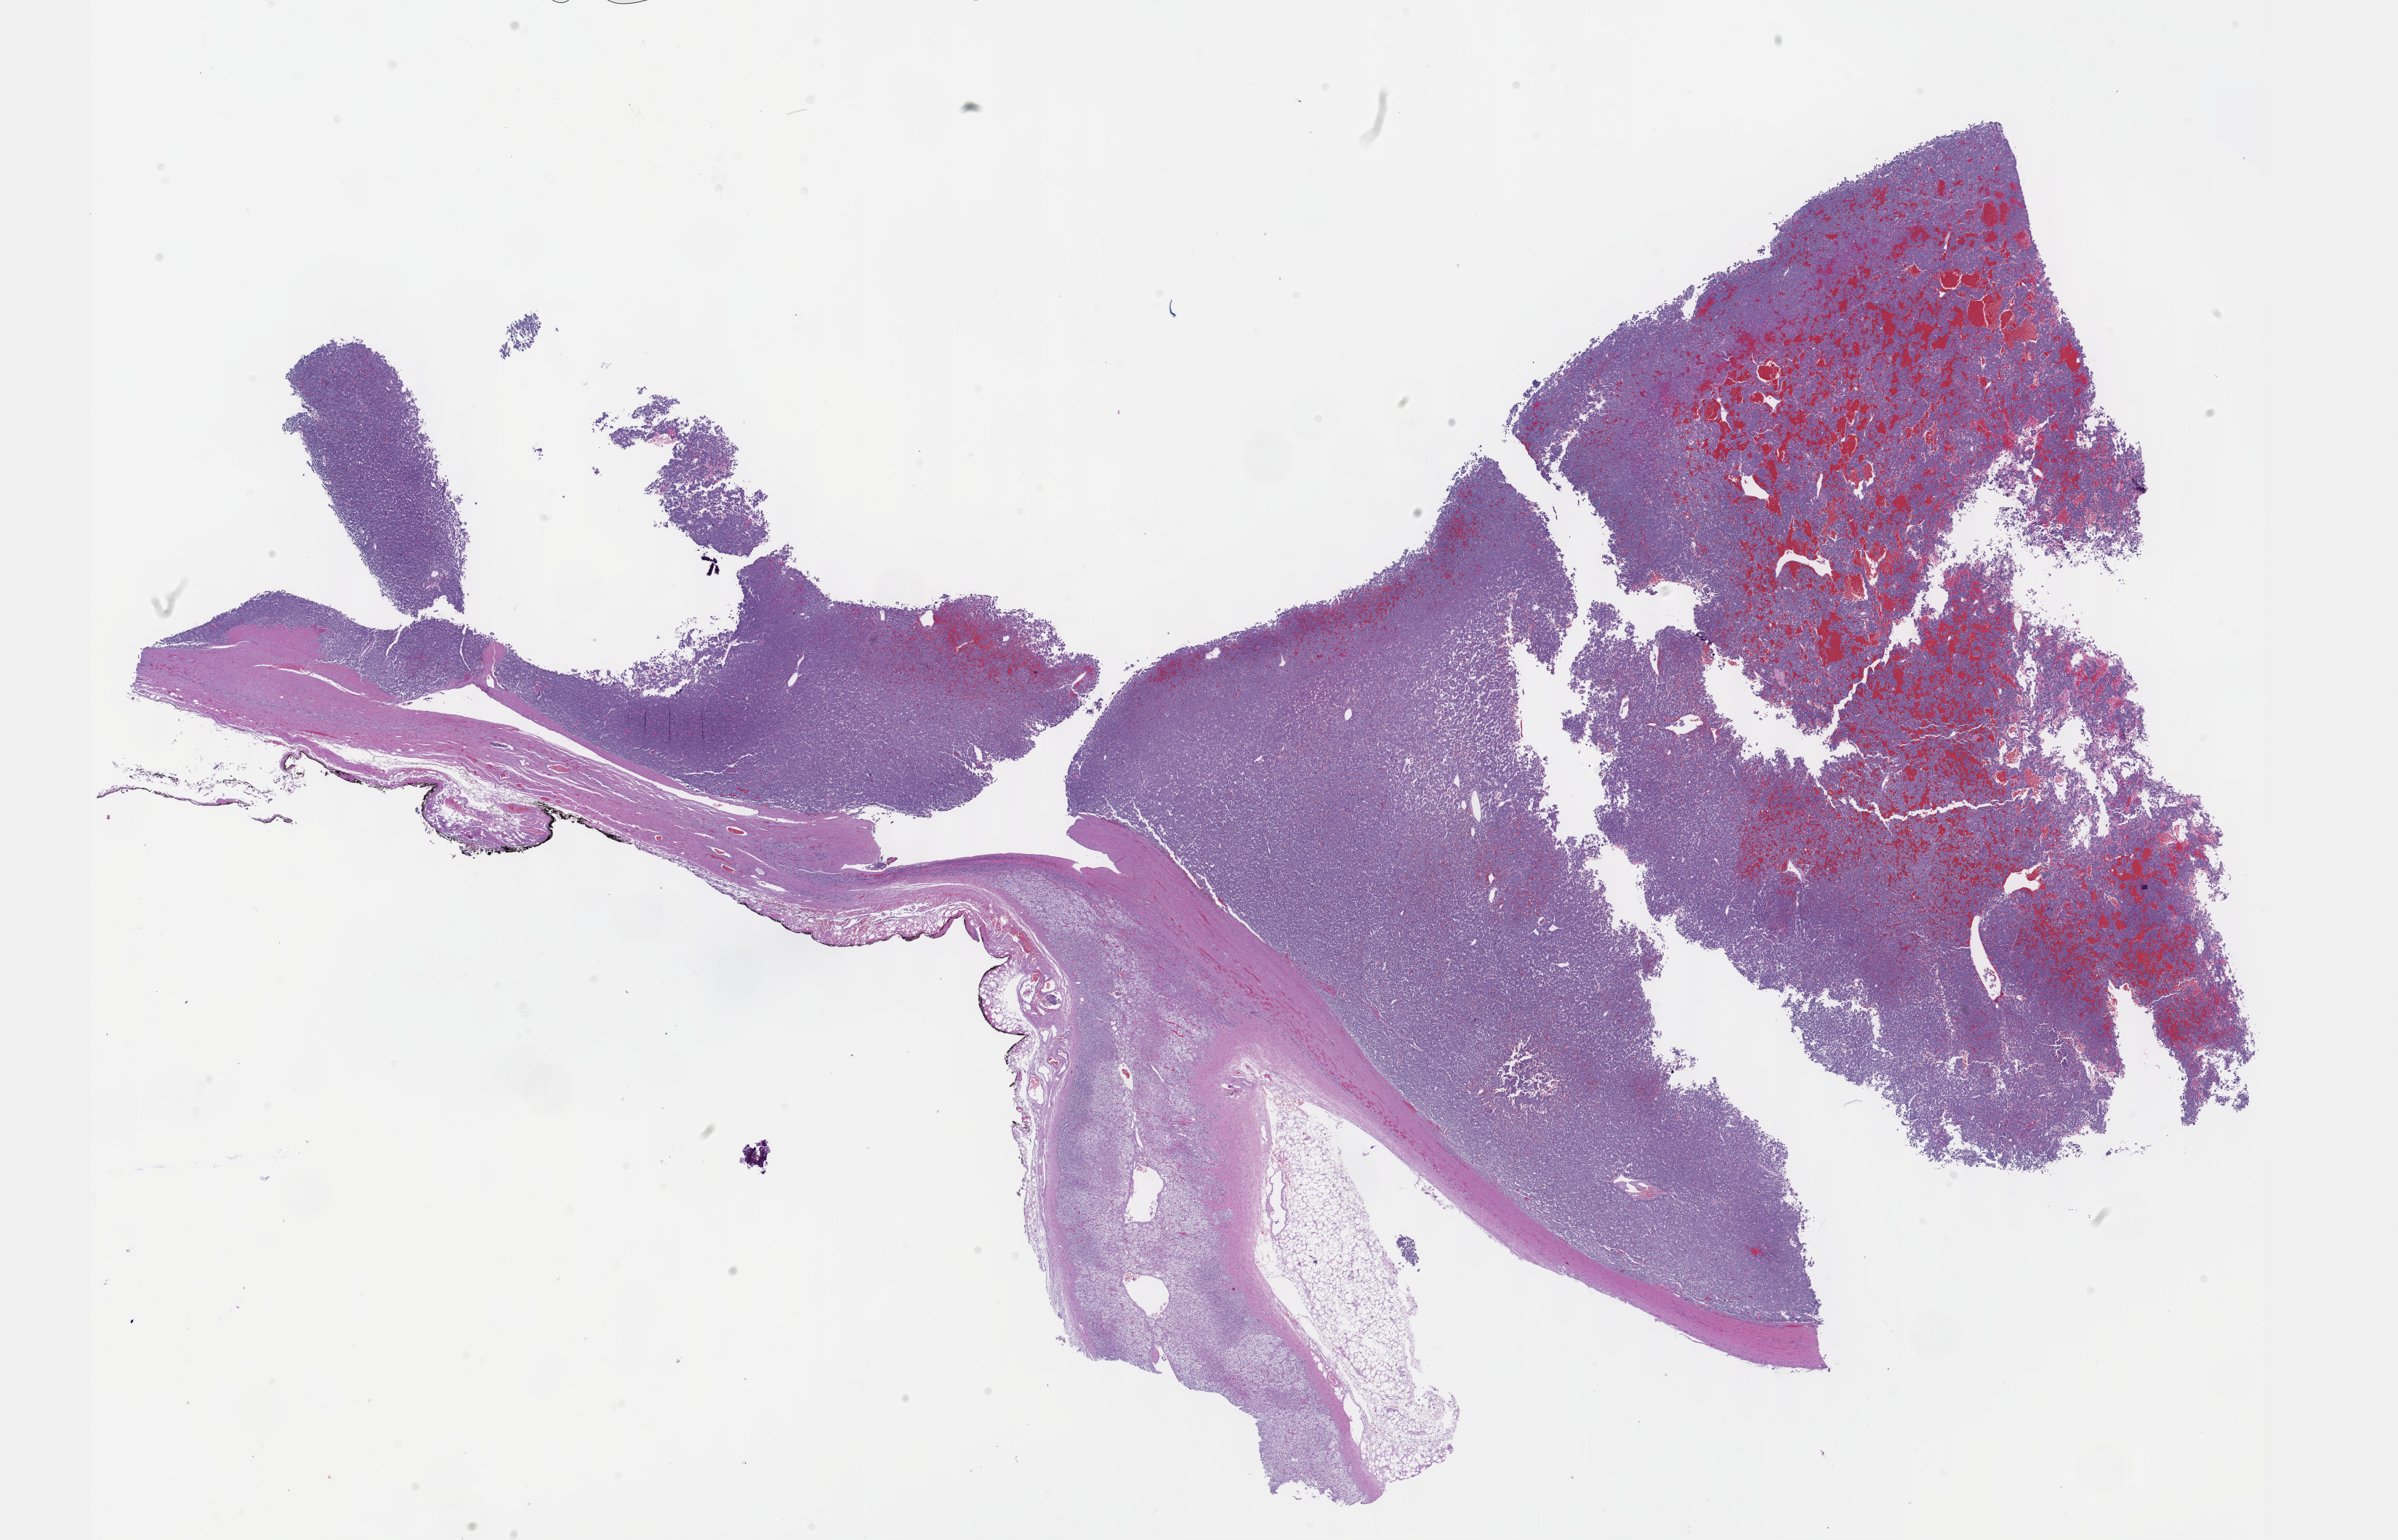
Digitized Hematoxylin and eosin (H&E) stained tissue section (whole slide) — whole scanned area (about 26.7 x 17.1 mm) shown as a low-resolution overview, formalin-fixed paraffin-embedded (FFPE) diagnostic section, adrenal gland, primary tumour sample. Female, age 66 years at initial diagnosis.
Laterality: right. Pathologic diagnosis: Pheochromocytoma, NOS.